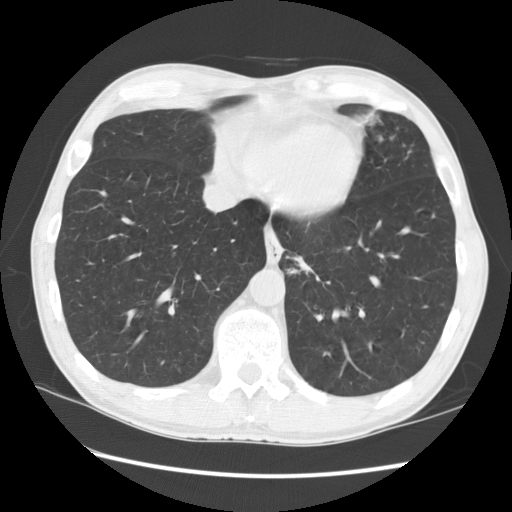
Low-dose screening chest CT, one axial slice; slice 36 of 141 in the series (ordered by position); 120 kVp; lung window (W 1500 / L -600 HU); 512 × 512 image matrix, field of view 360 × 360 mm.
Outlined on this slice (expert manual segmentation):
- lesion 1 (tumor, lower lobe of left lung): box from (x=376, y=115) to (x=377, y=119) px